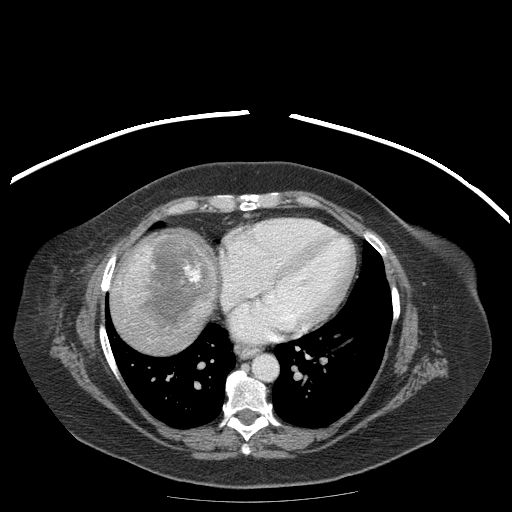
Contrast-enhanced abdominal CT (liver protocol), one axial slice; 120 kVp; soft-tissue window (W 400 / L 40 HU); 512 × 512 image matrix, field of view 440 × 440 mm. From the clinical record (not read from this slice): diagnosis: hepatocellular carcinoma (patient treated with transarterial chemoembolisation; whether this scan precedes or follows treatment is not stated here); TNM stage (as recorded): Stage-IIIB; Child-Pugh class: A.
Annotated regions visible in this slice (semi-automatic segmentation, software-assisted and operator-edited):
- liver parenchyma outside the tumour (the mass and vessels are separate outlines, so this box may not span the whole liver): box from (x=110, y=232) to (x=214, y=352) px
- mass: (x=119, y=235)–(x=215, y=329)